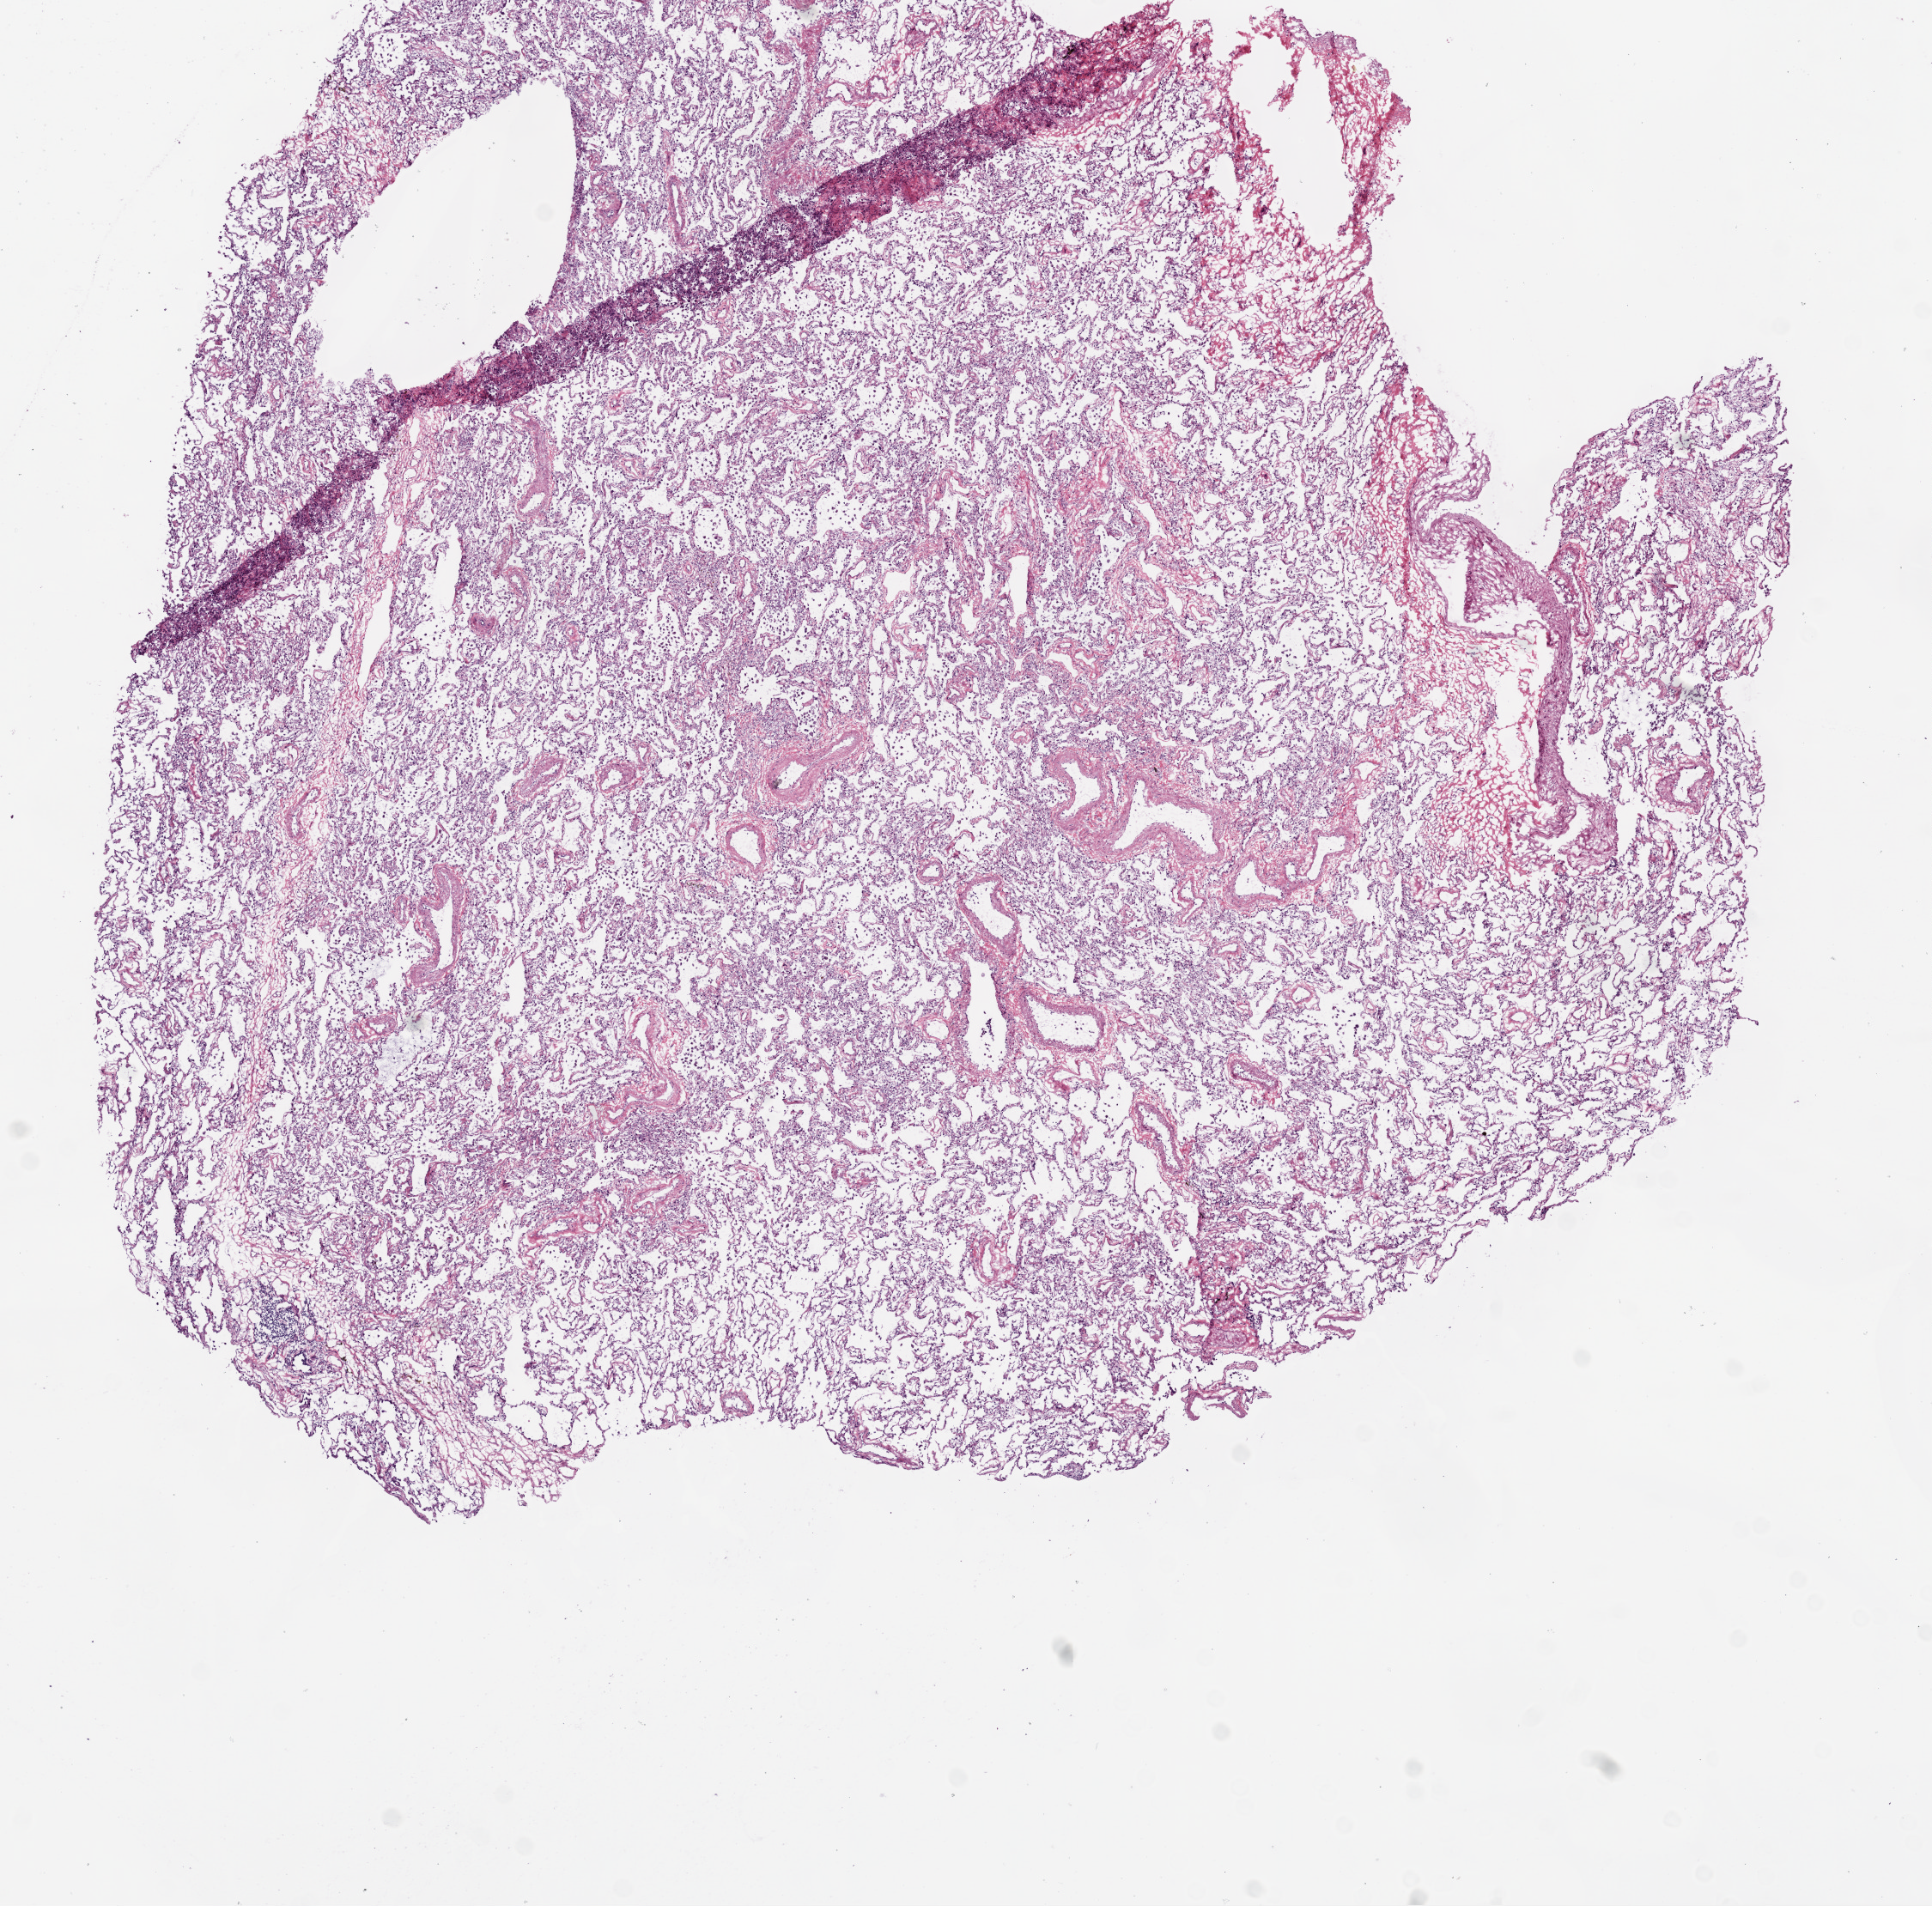
H&E-stained whole-slide image, shown as a low-resolution overview of the whole scanned area (about 9.0 x 8.9 mm). Frozen section. Sample: solid tissue normal (non-tumour tissue), lung. Female patient; age at initial diagnosis 64 years.
This section: solid tissue normal sample (biorepository sample class). Patient diagnosis: Adenocarcinoma, NOS (upper lobe, lung).